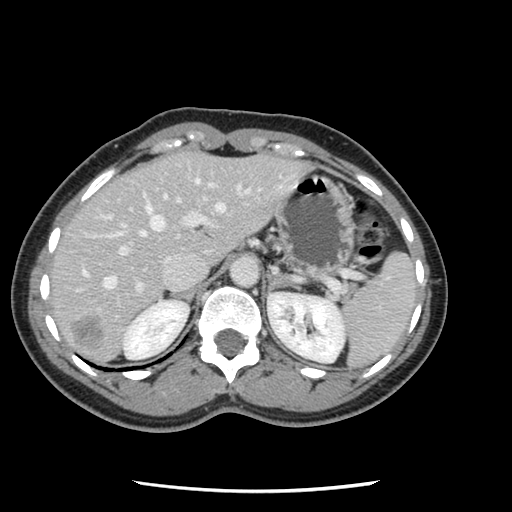
Contrast-enhanced abdominal CT, one axial slice; slice 85 of 134 in the series (ordered by position); 120 kVp; intravenous contrast given; soft-tissue window (W 400 / L 40 HU); 512 × 512 image matrix, field of view 330 × 330 mm. Female patient, age 43 years. Case-level facts recorded for this patient, not image findings: diagnosis: colorectal cancer liver metastases, imaged before liver resection; multiple liver metastases: yes; largest metastasis: 3.4 cm; disease in both lobes: yes.
Structures marked on this image (manually delineated by an expert):
- hepatic veins: box from (x=77, y=178) to (x=247, y=291) px
- liver: (x=50, y=153)–(x=306, y=364)
- planned liver remnant (the part of the liver to remain after resection): (x=50, y=156)–(x=190, y=308)
- portal vein (with intrahepatic branches): (x=96, y=183)–(x=283, y=294)
- liver metastasis: (x=71, y=316)–(x=105, y=347)